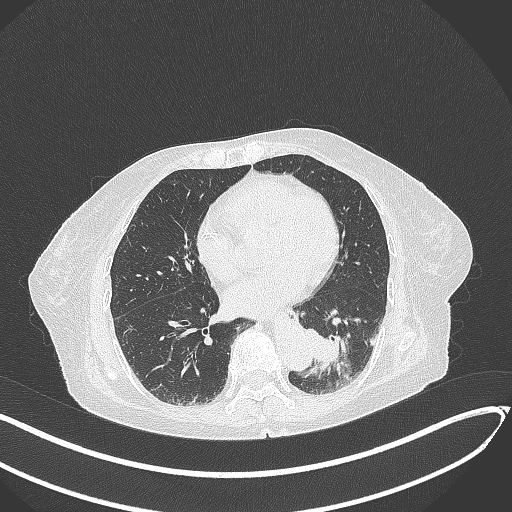
Chest CT, one axial slice; position 96 of 324 along the scan axis; reconstruction kernel B70f; lung window (W 1500 / L -600 HU); 512 × 512 image matrix, field of view 400 × 400 mm. Patient: female, 82 years. From the clinical record (not read from this slice): clinical TNM (as recorded): T1b N0 M1.
Annotated regions visible in this slice (rectangle marked by the reading radiologist):
- lung tumour (recorded histology: adenocarcinoma): bounding box (x1, y1, x2, y2) in pixels: (301, 324, 350, 372)